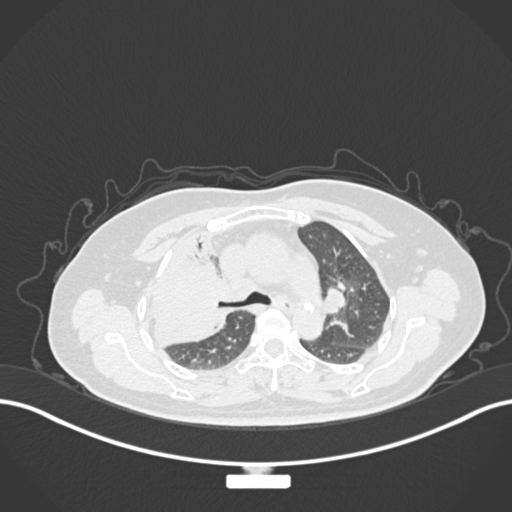
Chest CT, one axial slice; position 106 of 177 along the scan axis; reconstruction kernel B30f; lung window (W 1500 / L -600 HU); 1 mm slice thickness; 512 × 512 image matrix, field of view 400 × 400 mm. Female patient, age 60 years. Case-level facts recorded for this patient, not image findings: clinical TNM (as recorded): T3 N1 M1.
Annotated regions visible in this slice (rectangle marked by the reading radiologist):
- lung tumour (recorded histology: adenocarcinoma): bounding box <151,243,237,355> (left, top, right, bottom; pixels)